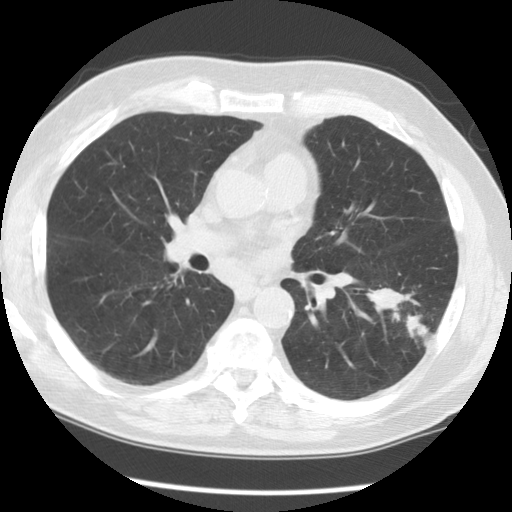
Chest CT (low-dose screening protocol), one axial image, first (baseline) screen, lung window (W 1500 / L -600 HU), 120 kVp, 512 × 512 image matrix. Male, age 71 years at enrolment.
Expert-annotated lung lesion, bounding box <369,274,460,365> (left, top, right, bottom; pixels). The screening reader recorded 3 non-calcified nodules or masses ≥4 mm on this exam (left lower lobe, right upper lobe, right upper lobe); which of them this box marks is not recorded. Participant outcome: lung cancer diagnosed 42 days after this screen — small cell carcinoma, NOS, left lower lobe, poorly differentiated (G3), stage IIIA (AJCC 6th edition), 19 mm at pathology.